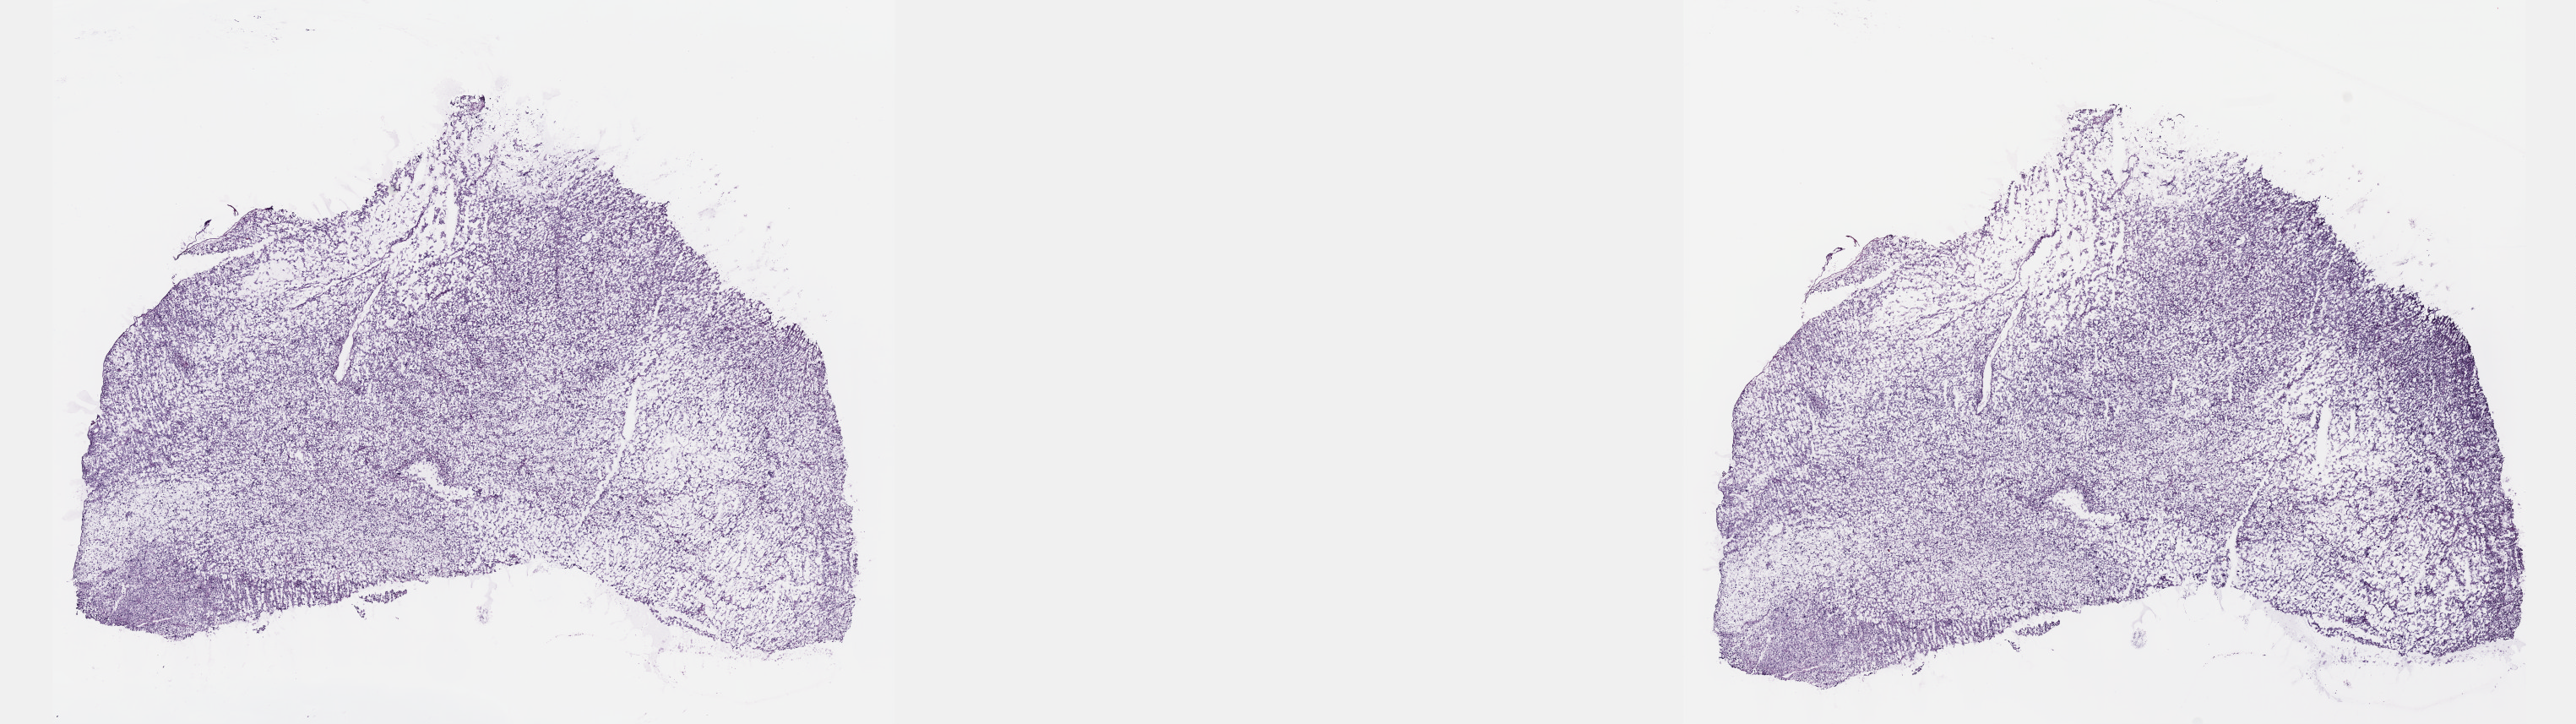
Digitized H&E tissue section (whole slide), low-resolution overview of the scanned area, about 24.6 x 6.9 mm (from a 40x scan). Frozen section. Connective, subcutaneous and other soft tissues, primary tumour sample. Patient: female, age at initial diagnosis 63 years. Slide review estimates, as recorded: tumour cells 80%, tumour nuclei 80%, normal cells 0%, stromal cells 20%, necrosis 0%. Inflammatory infiltration, as recorded: lymphocyte infiltration 3%, monocyte infiltration 1%, neutrophil infiltration 2%.
Pathologic diagnosis: Malignant fibrous histiocytoma (connective, subcutaneous and other soft tissues of lower limb and hip).